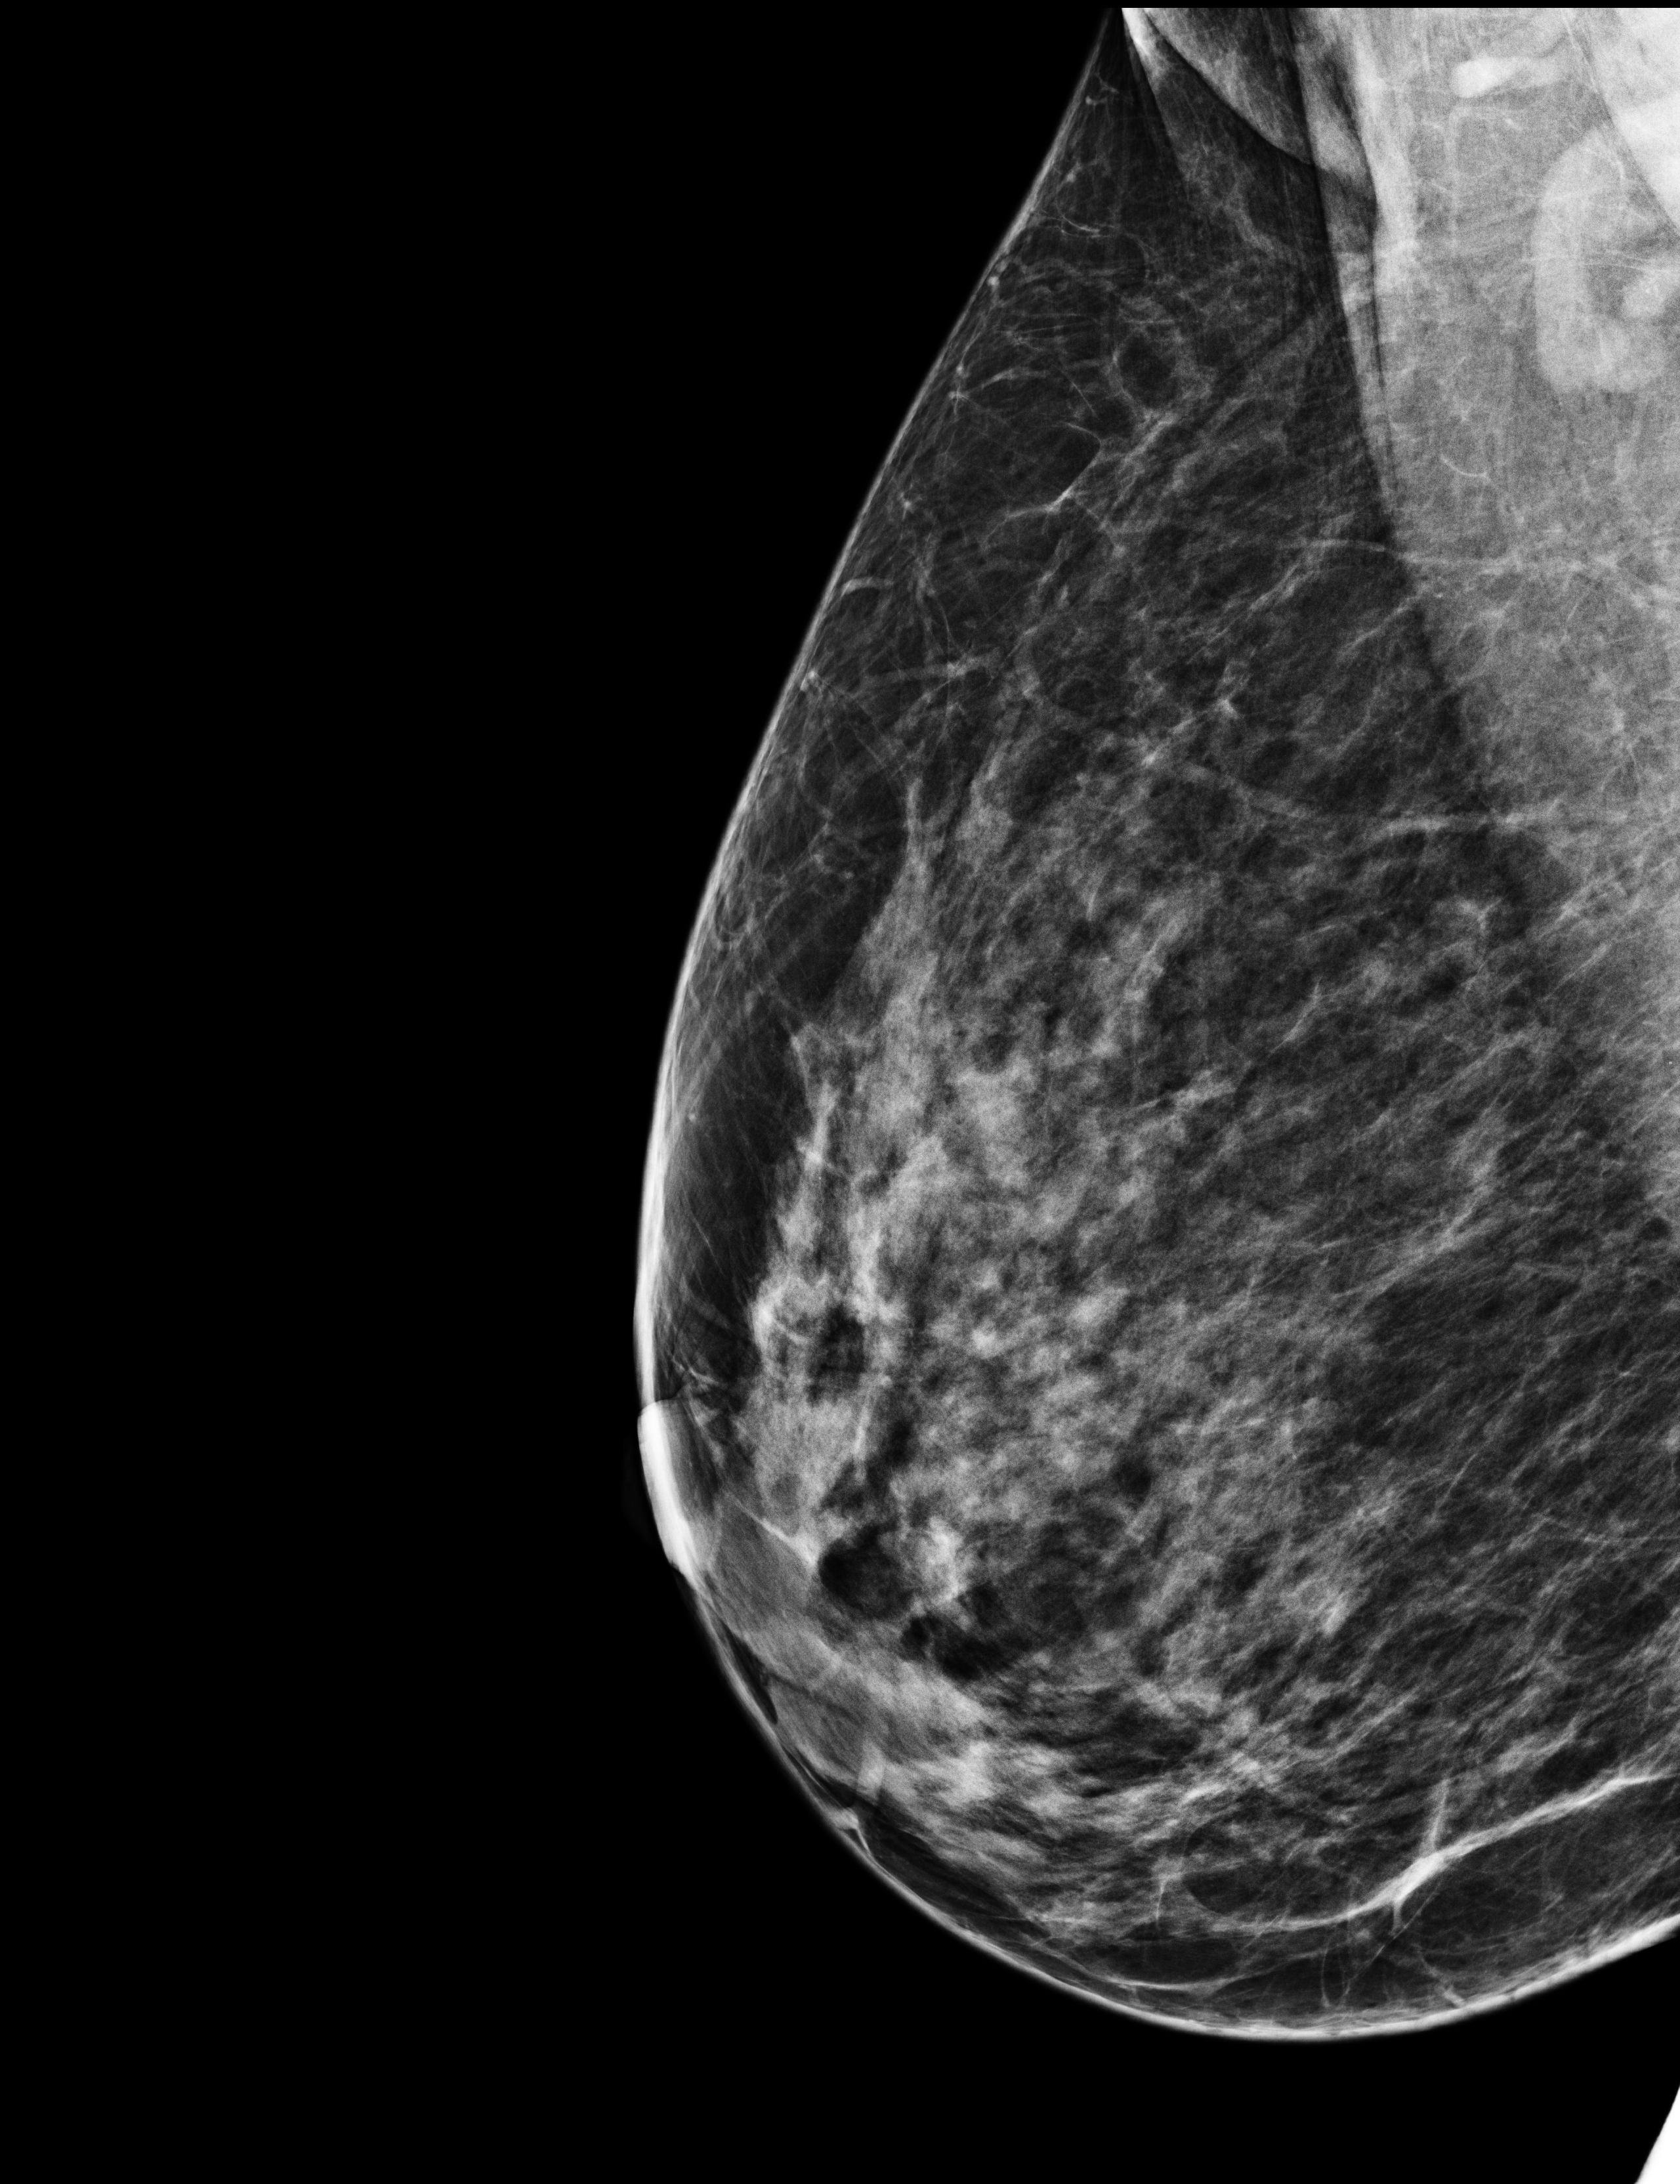
Screening examination. Patient: female, 43 years.
Image type: full-field digital mammogram. Breast: right. Projection: medio-lateral oblique projection. Breast density at the screening exam (both breasts): heterogeneously dense (BI-RADS density category c). Final BI-RADS assessment for this screening round (tomosynthesis exam, both breasts): category 1. Recall: no recall after this screen.